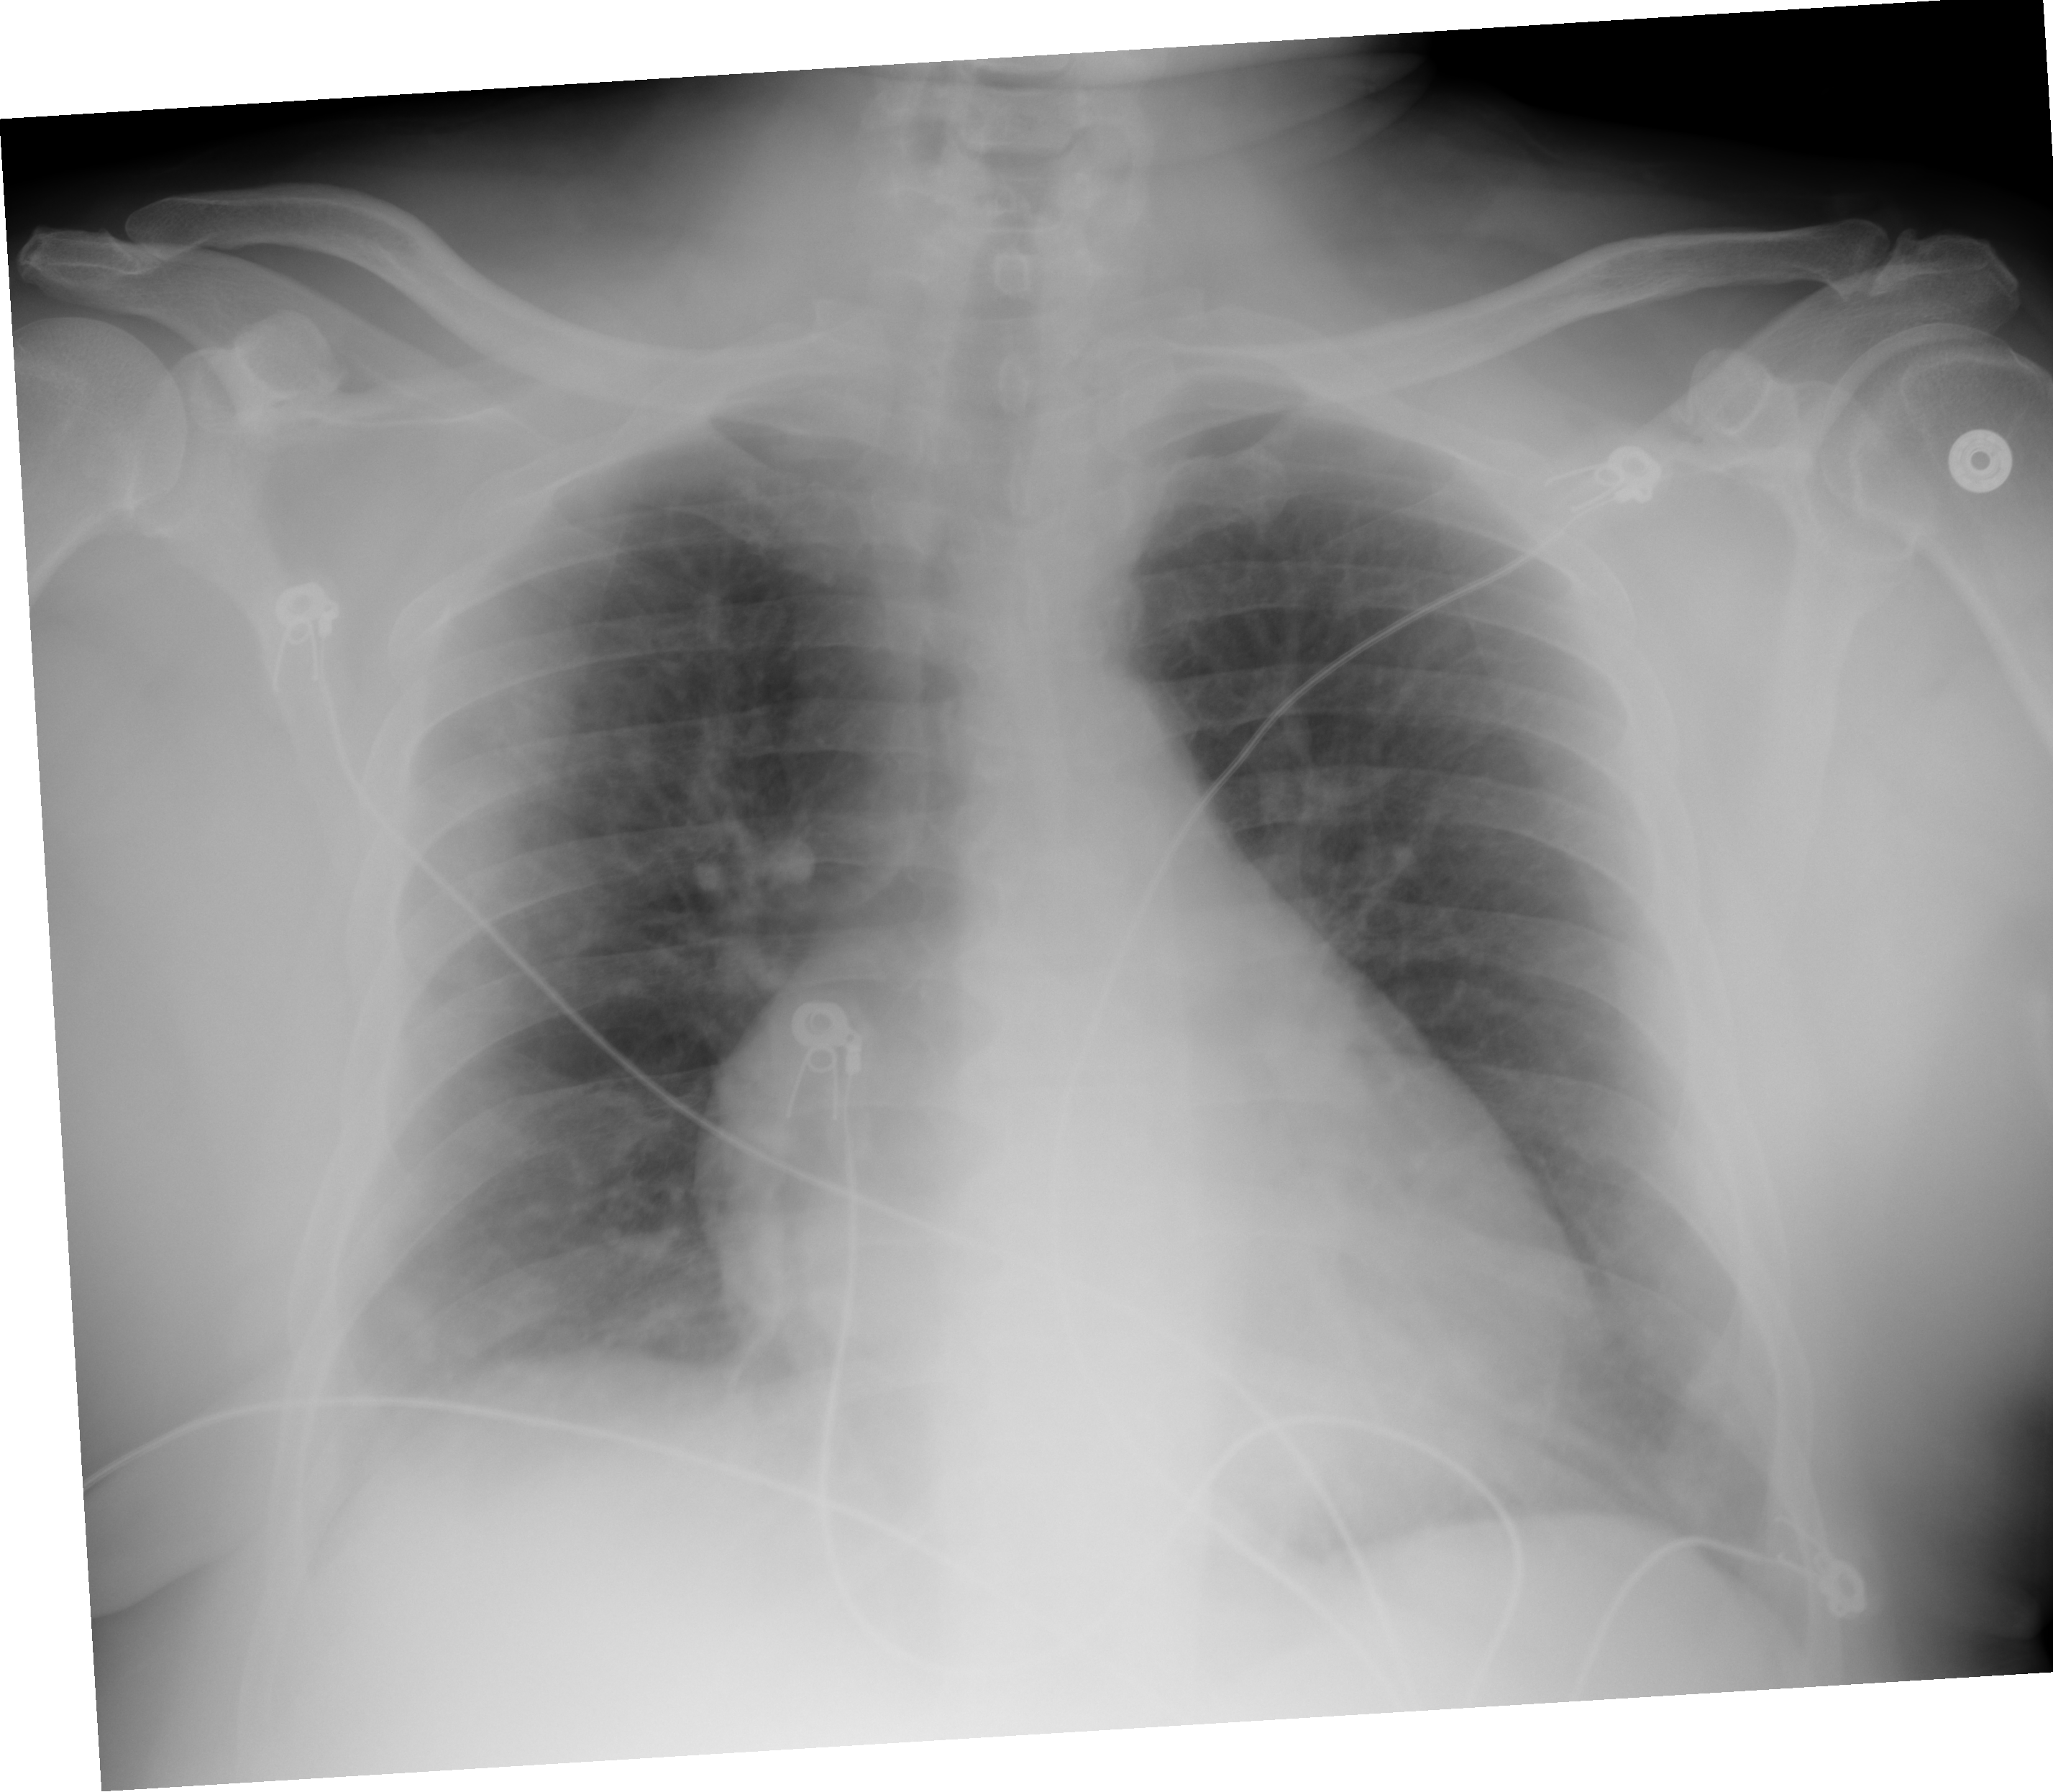
Chest X-ray (portable), AP projection. Male patient, age 51 years; COVID-19 (test-positive).
Key findings recorded by the radiologist: Subtle patchy bibasilar and right upper lobe airspace opacities.